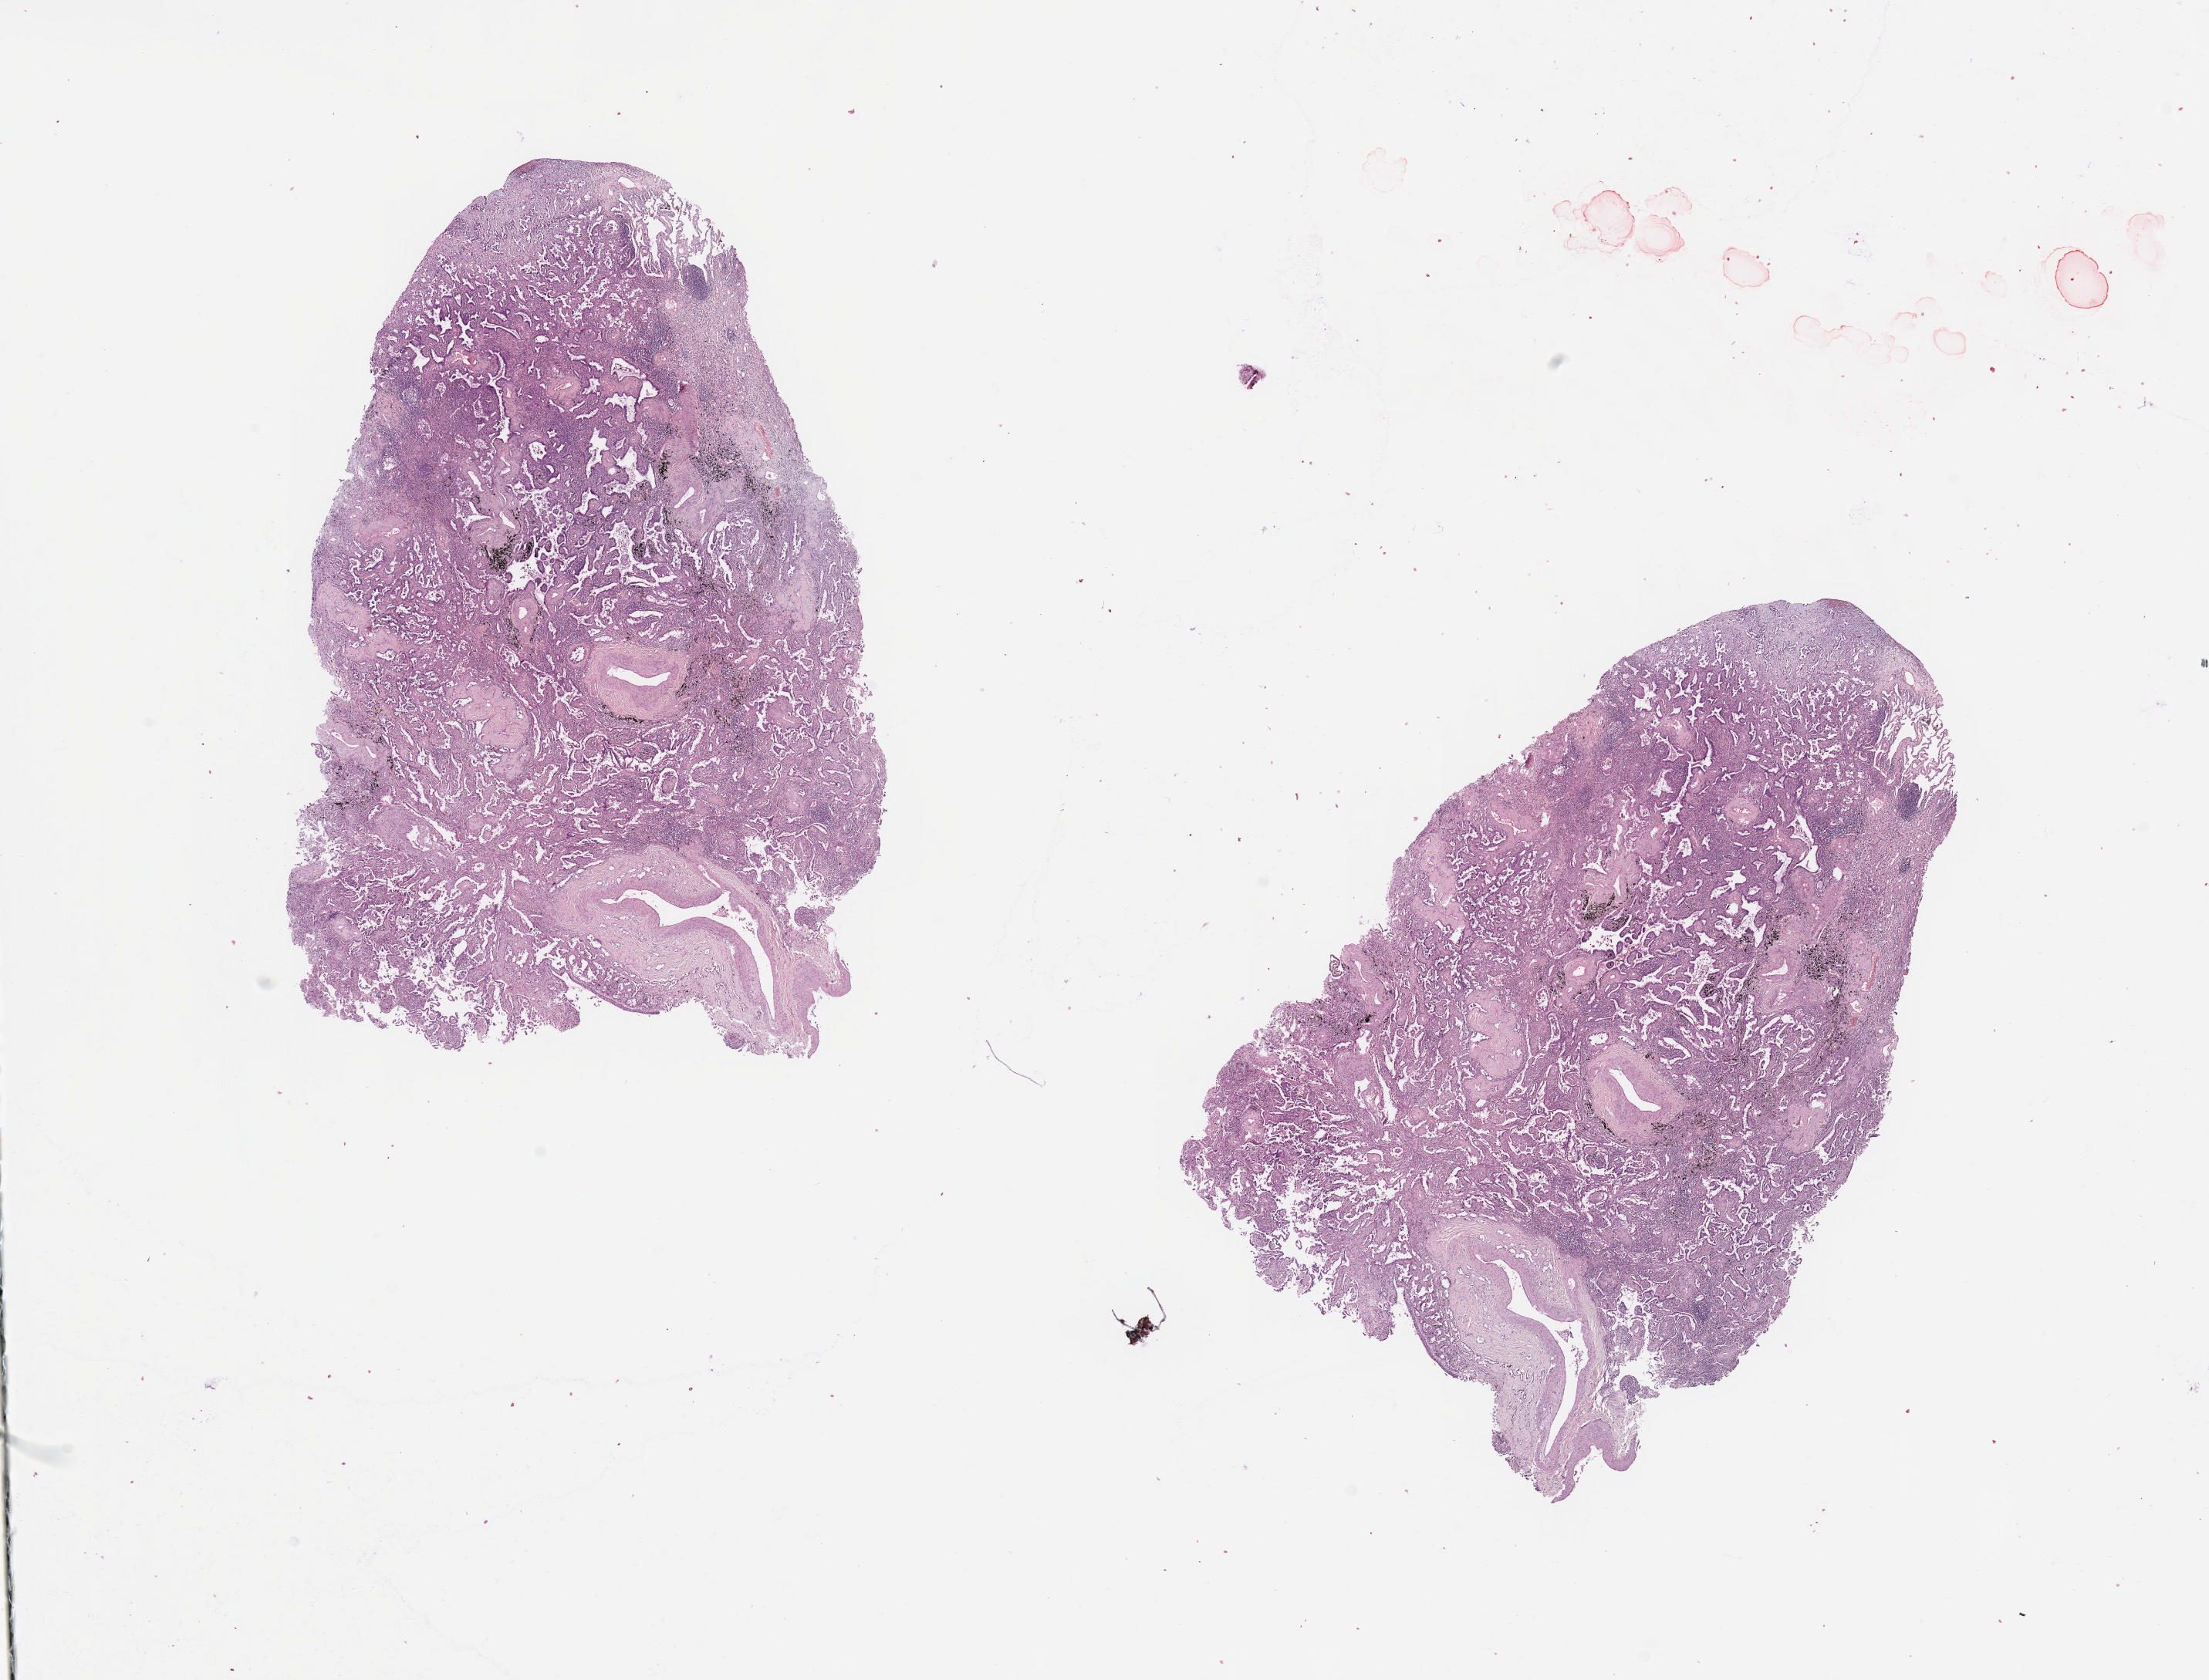
Hematoxylin and eosin (H&E) stained whole-slide image, shown as a low-resolution overview of the whole scanned area (about 22.6 x 17.2 mm); tumour tissue sample, sampled site: lung. 68-year-old male patient. Histologic grade: G2 (moderately differentiated). Composition of this section per pathologist review: tumour nuclei 60%, necrosis 0%.
* diagnosis: Adenocarcinoma, NOS
* AJCC pathologic stage: IA
* primary tumour site (as recorded): right middle lobe